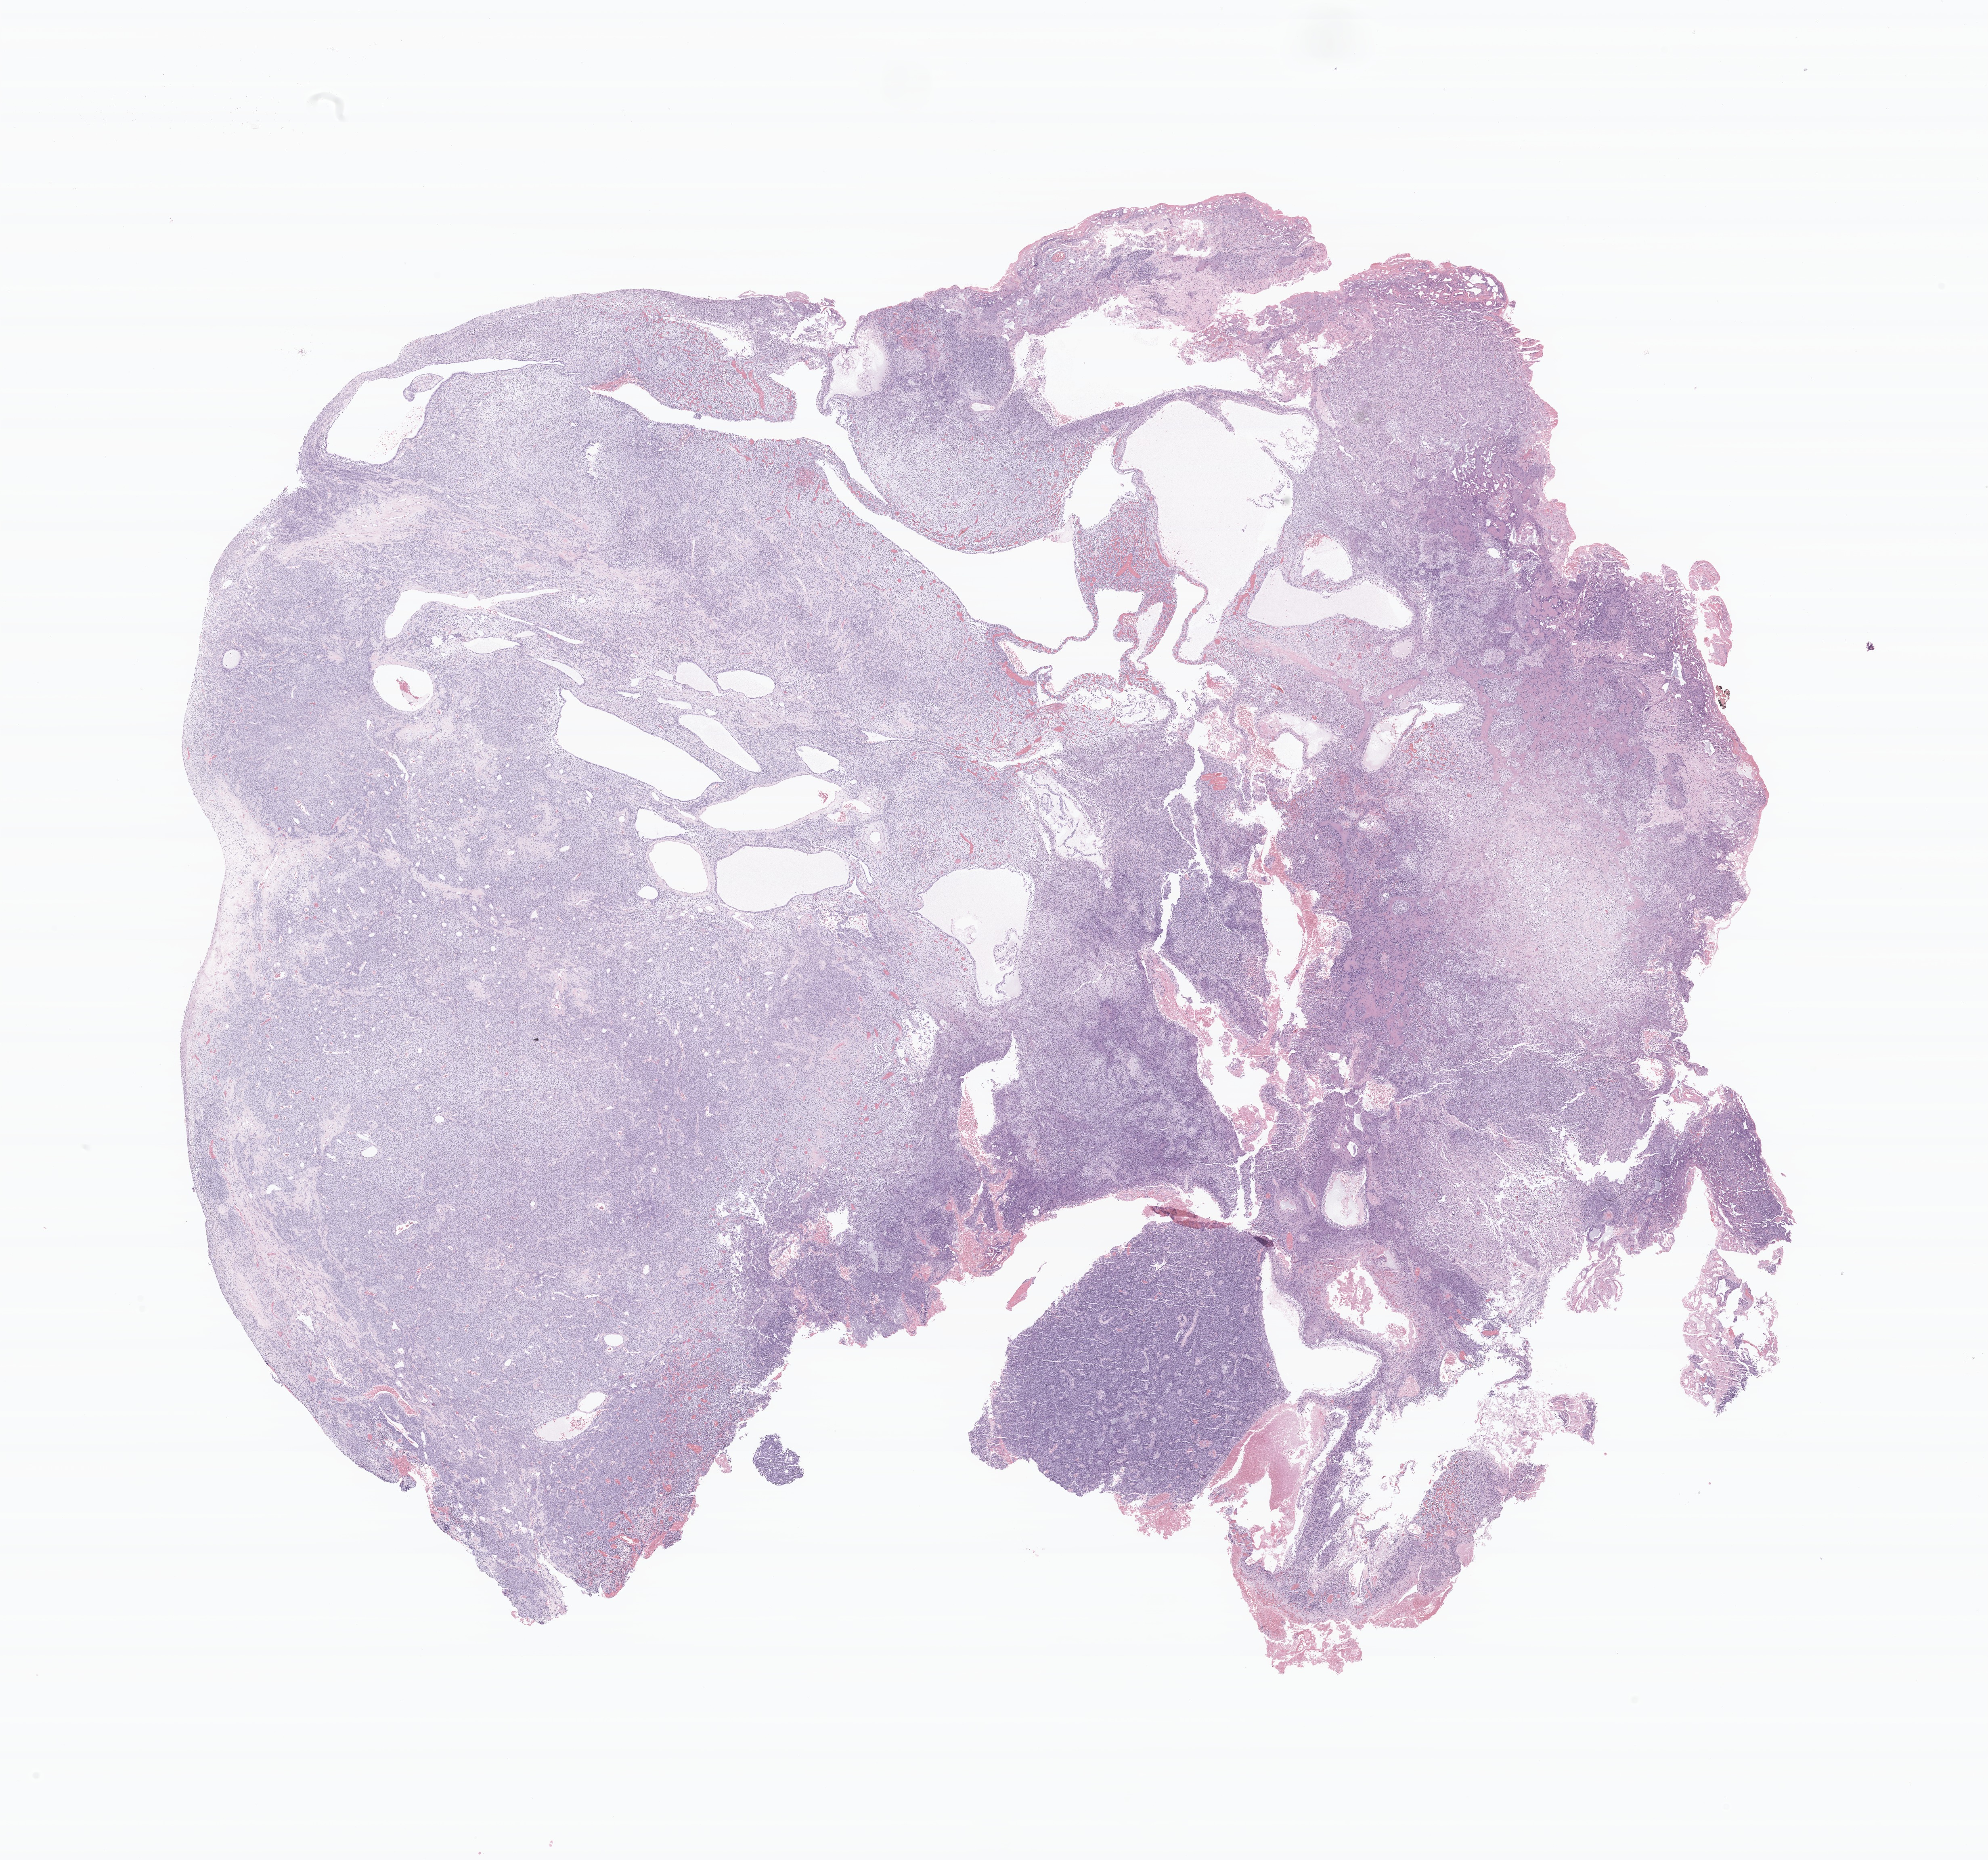
Digitized H&E-stained section of tumor tissue from the brain — shown as a low-resolution overview of the whole scanned area (about 20.8 x 19.4 mm); formalin-fixed paraffin-embedded section. Male patient, age 67 months (5 years 7 months).
Diagnosis (ICD-O-3 morphology term): Neoplasm, uncertain whether benign or malignant.